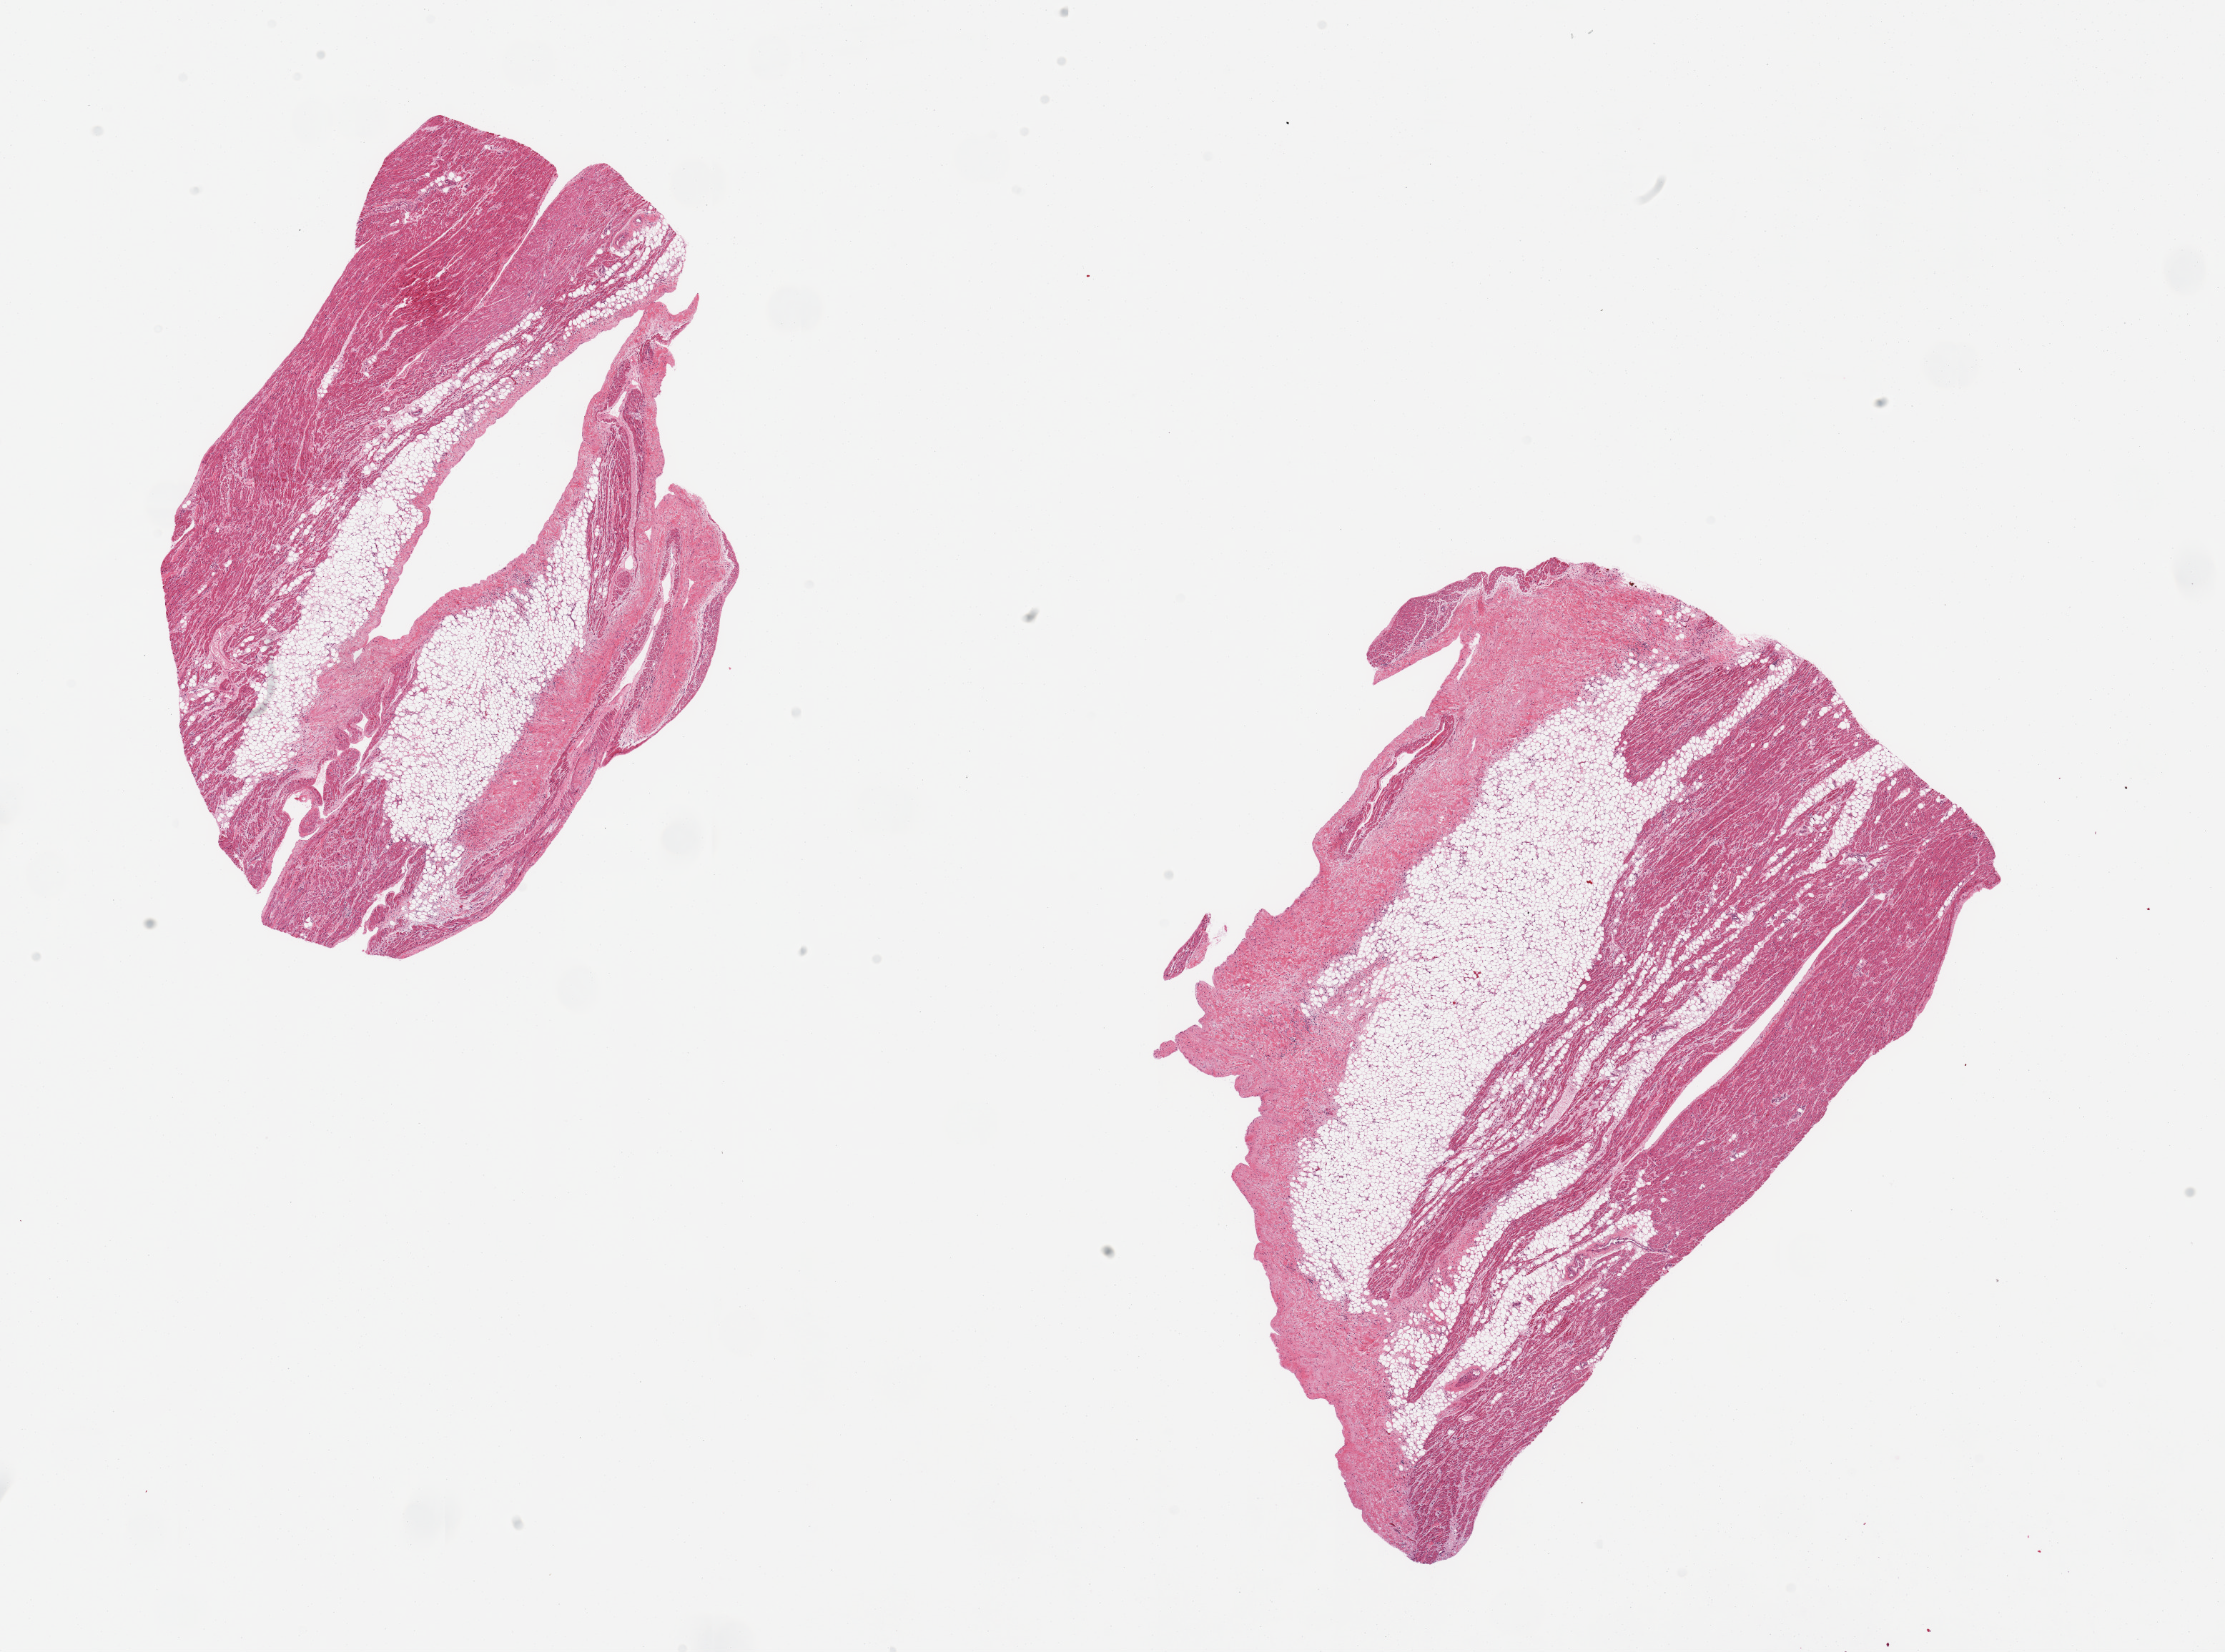
Hematoxylin and eosin (H&E) whole-slide image, shown as a low-resolution overview of the whole scanned area (about 24.6 x 18.3 mm); PAXgene-fixed, paraffin-embedded tissue; section of auricular appendage (target tissue); donor tissue sample.
Review note (as recorded): 2 pieces, each ~50-60% fat/fibrous tissue.